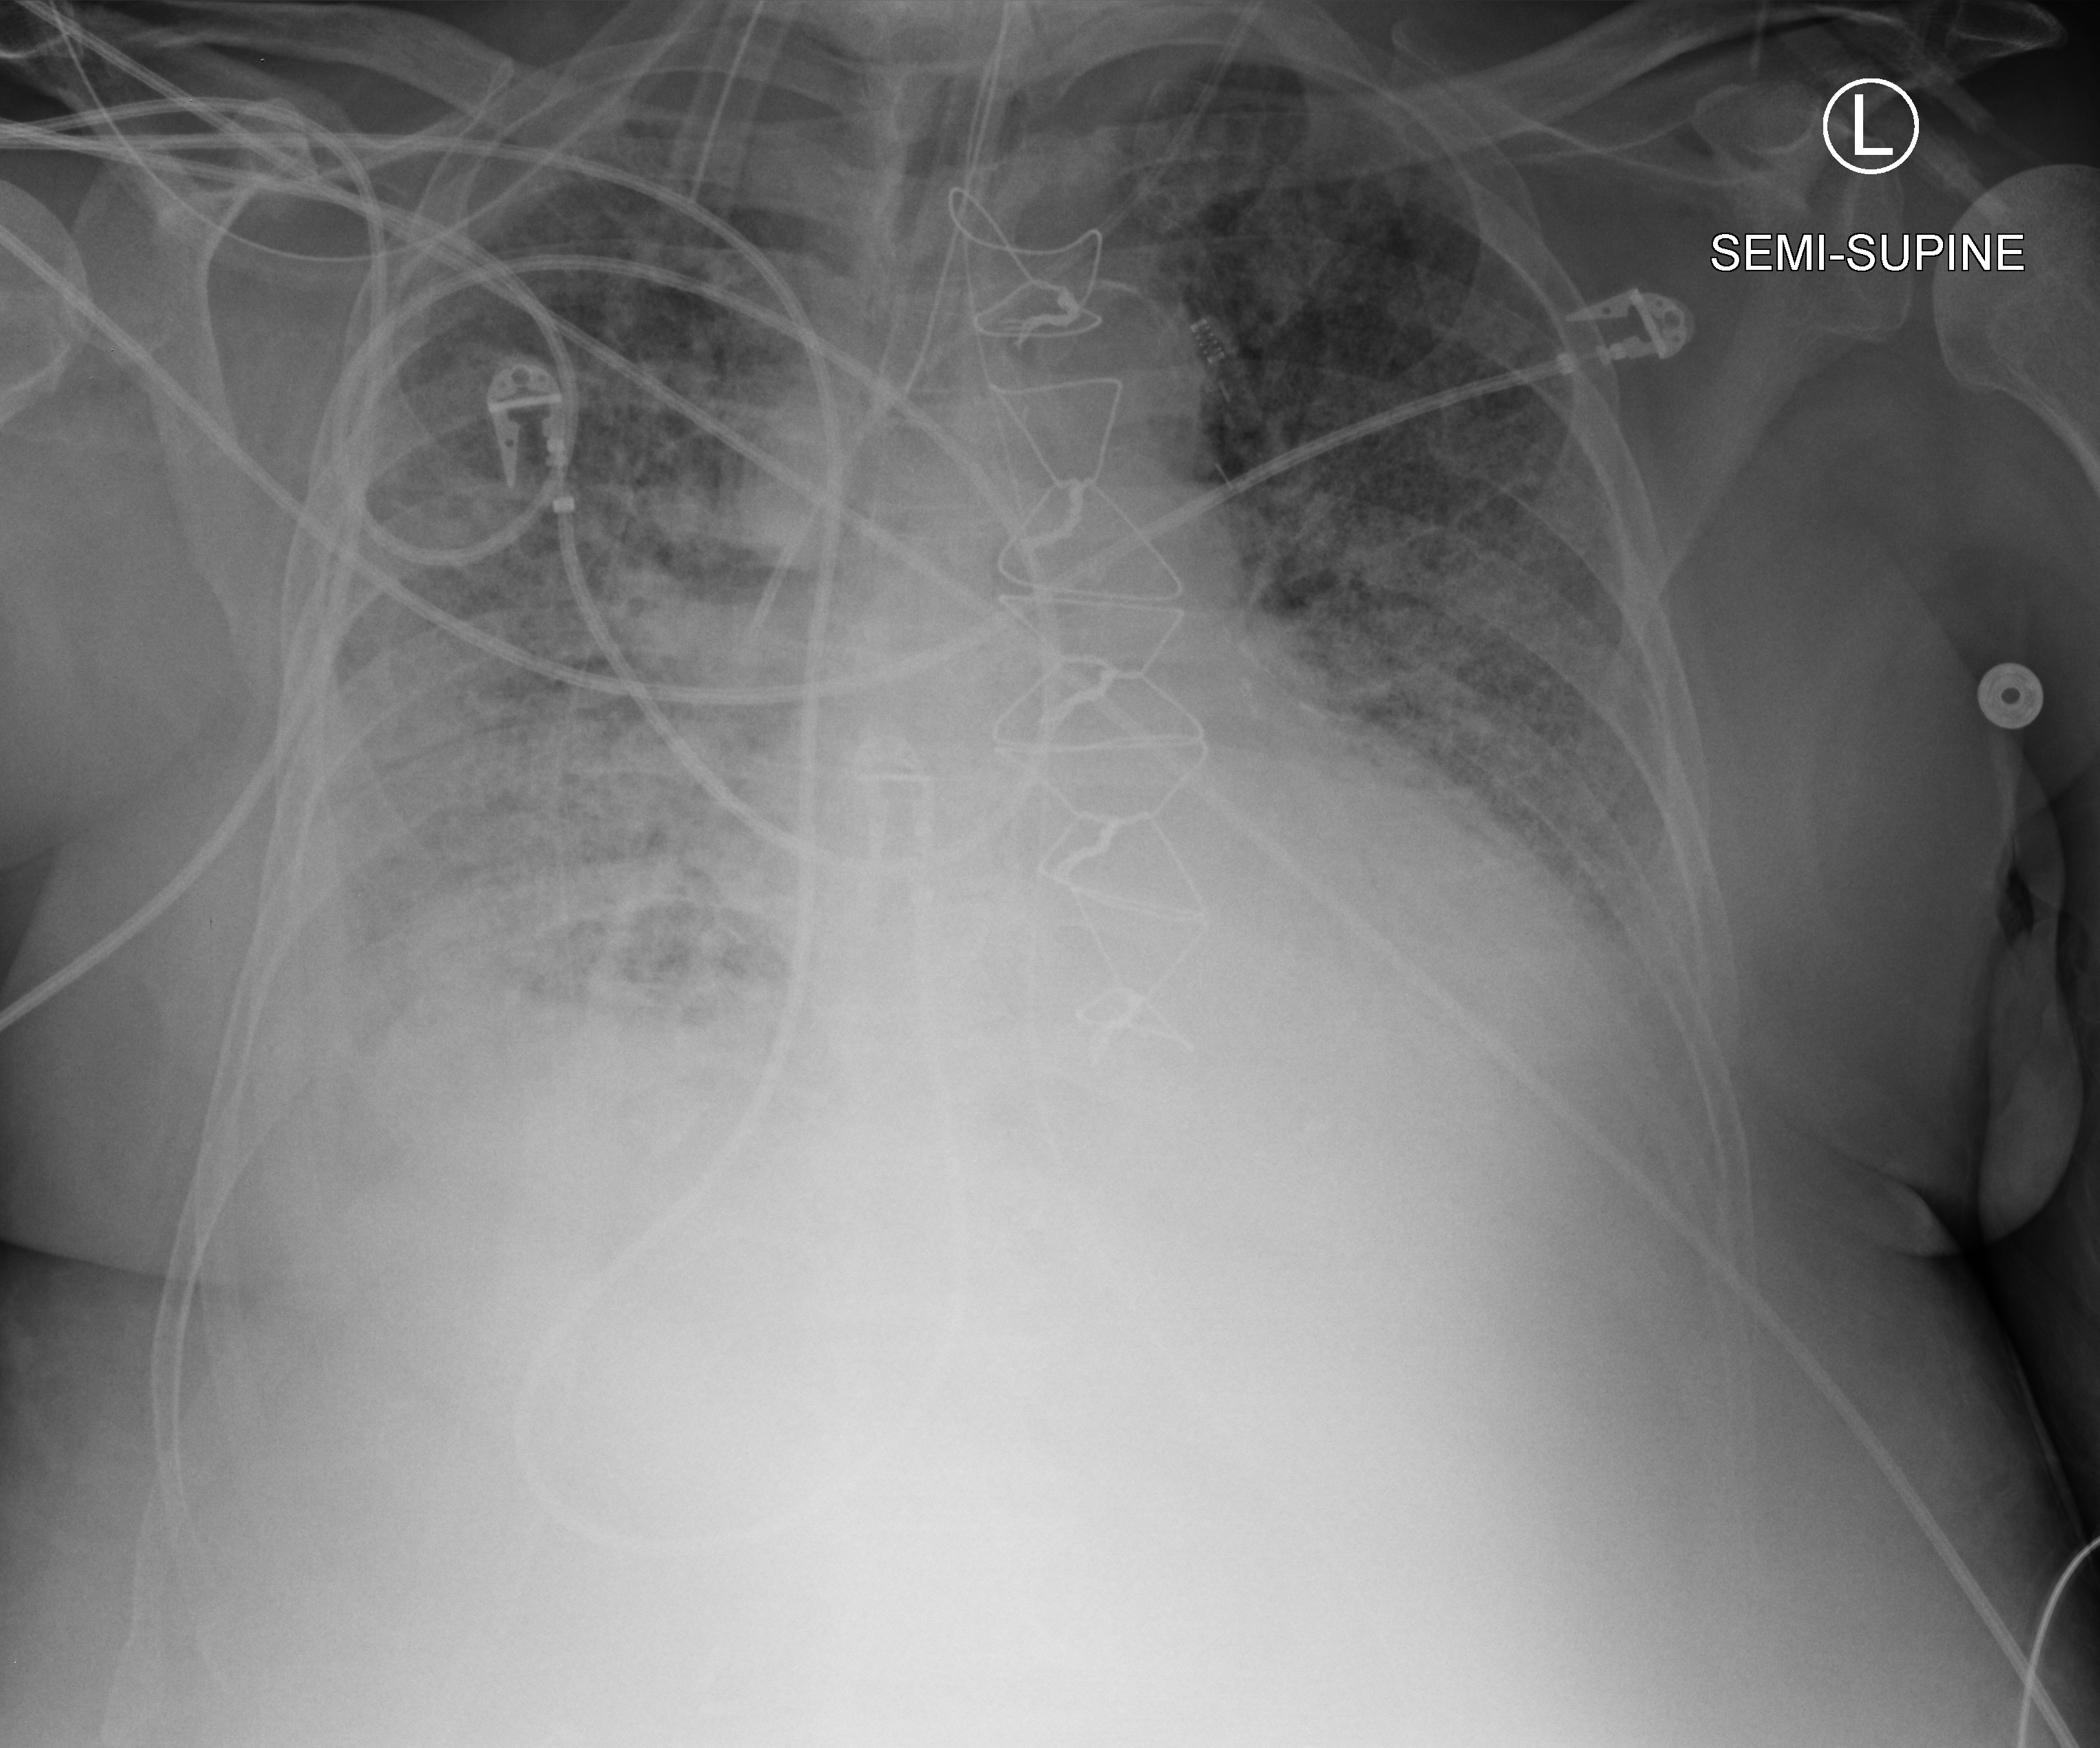
Bedside chest radiograph (computed radiography), anteroposterior (AP) projection. Male patient hospitalised with COVID-19, age 75–90 years.
Admission-level facts for this patient (not findings on this image; timing relative to this image not recorded): smoking status (admission record): never; mechanically ventilated during this hospital stay: yes; length of hospital stay: 28 days.